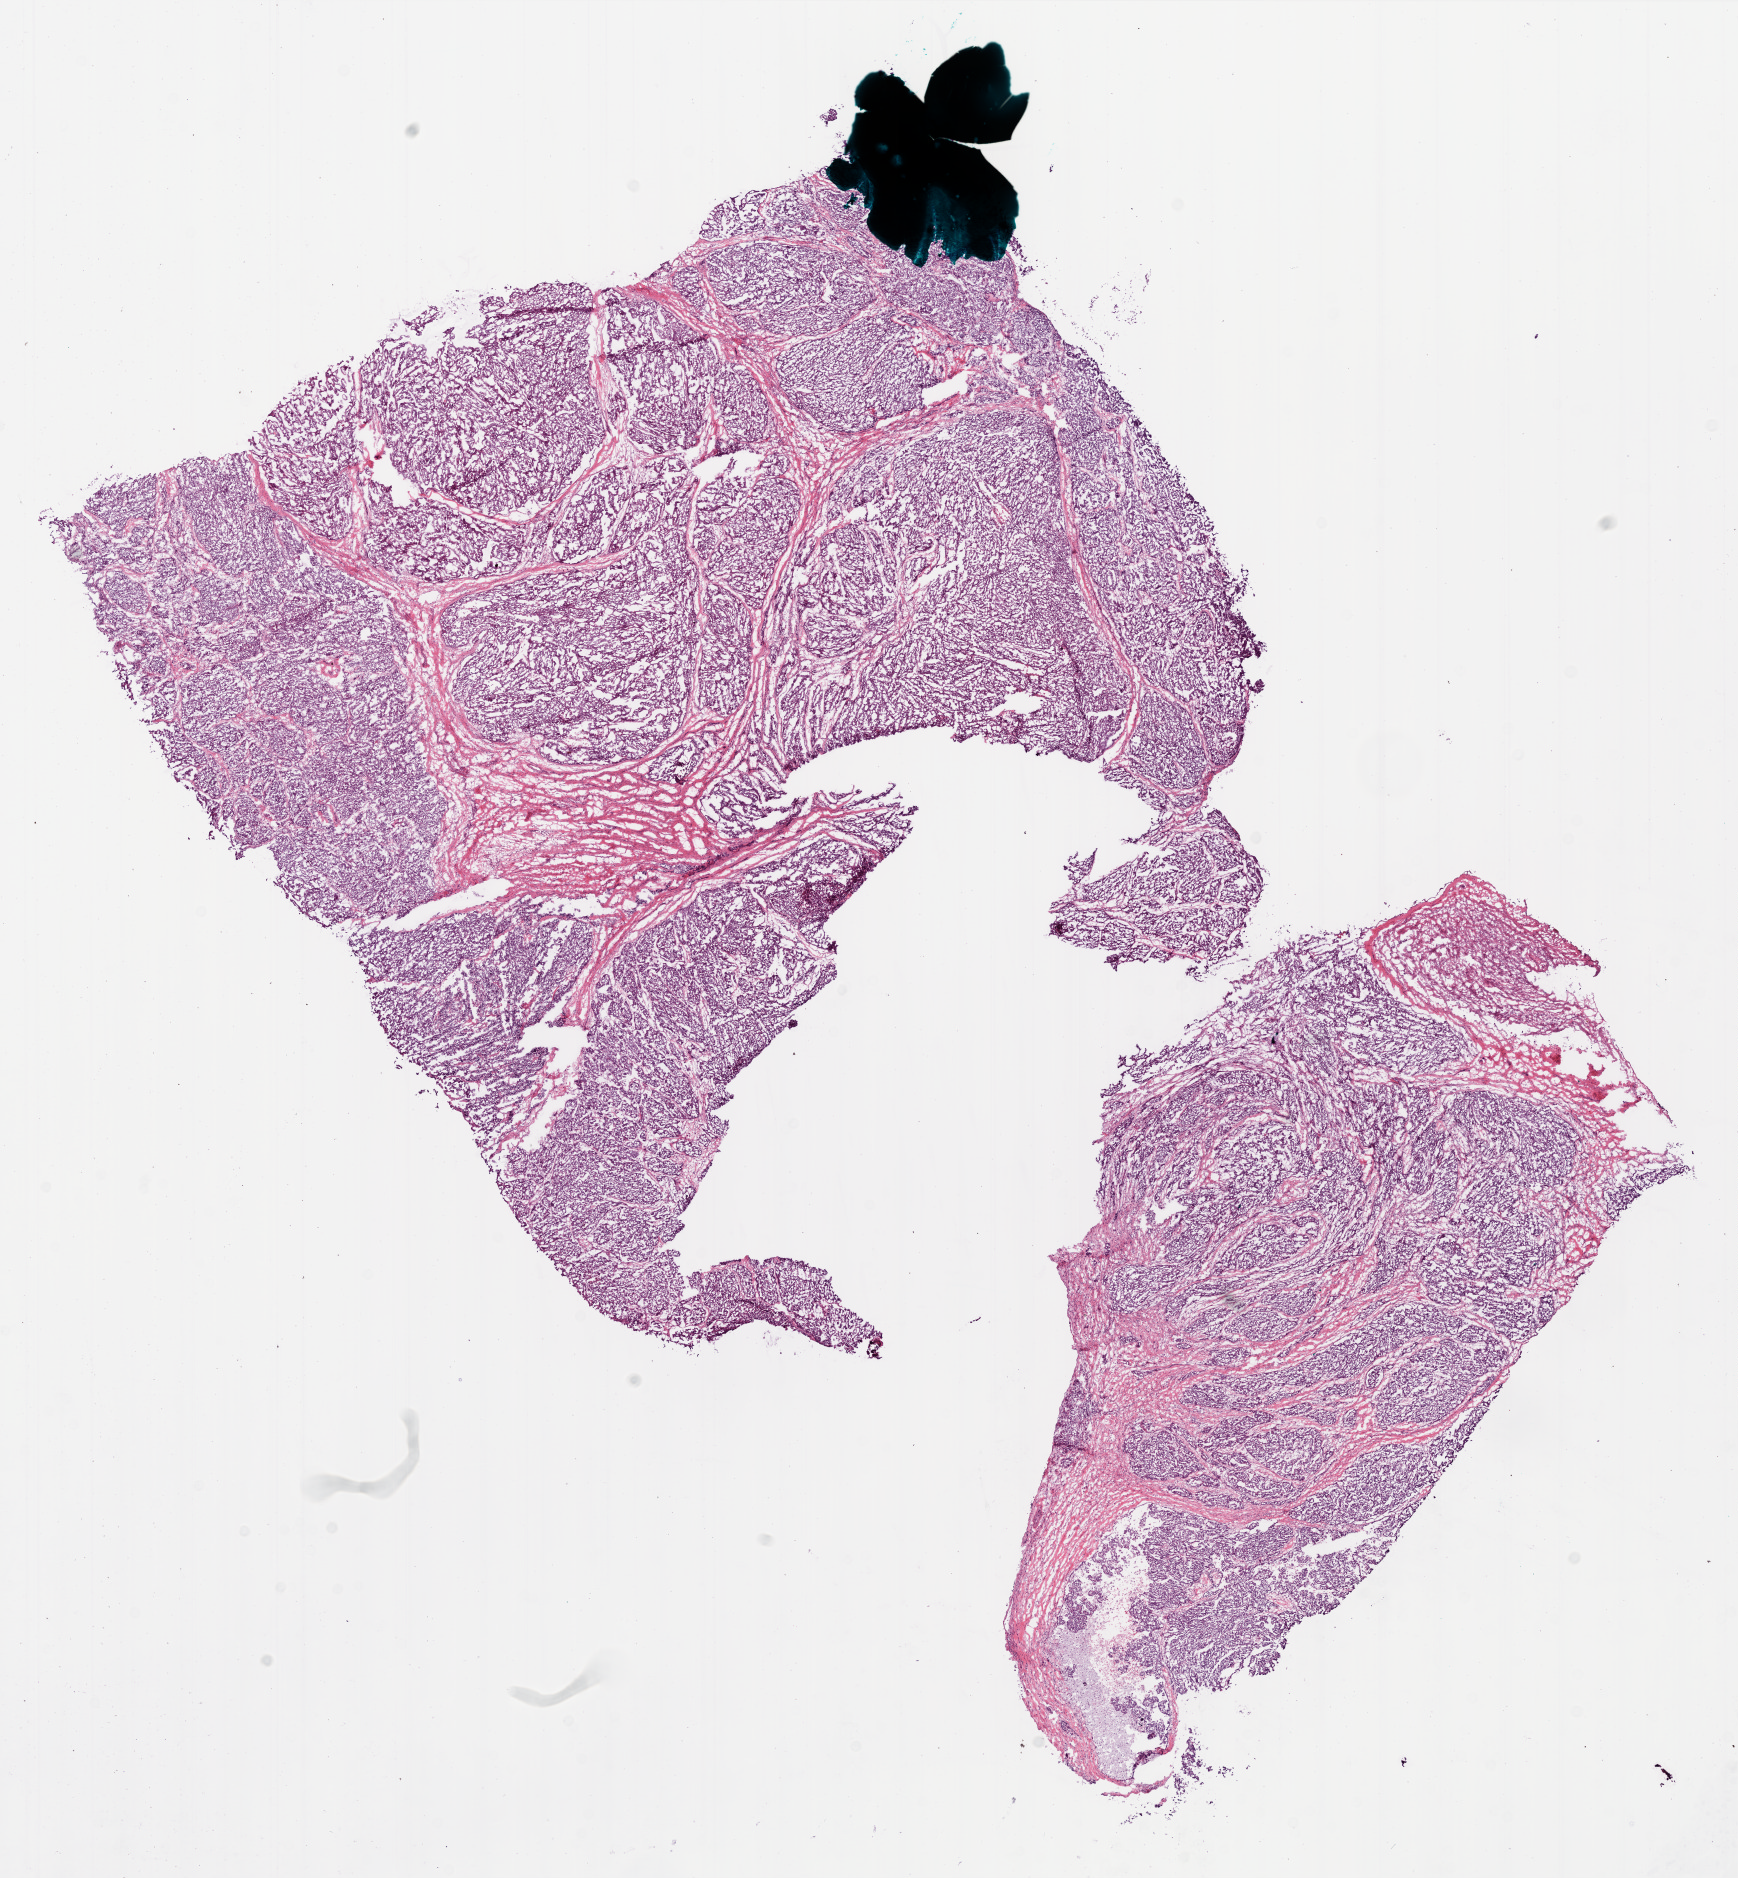
Whole-slide histology image, Hematoxylin and eosin (H&E) stained — whole scanned area (about 14.0 x 15.1 mm, from a 20x scan) shown as a low-resolution overview, frozen section, ovary, primary tumour sample. Female, age 81 years at initial diagnosis. Histologic grade: G3 (poorly differentiated). Pathologist review of this section (percent, as recorded): tumour cells 85%, tumour nuclei 90%, normal cells 0%, stromal cells 15%, necrosis 0%.
FIGO stage: IIIC. Histologic diagnosis: Serous cystadenocarcinoma, NOS.